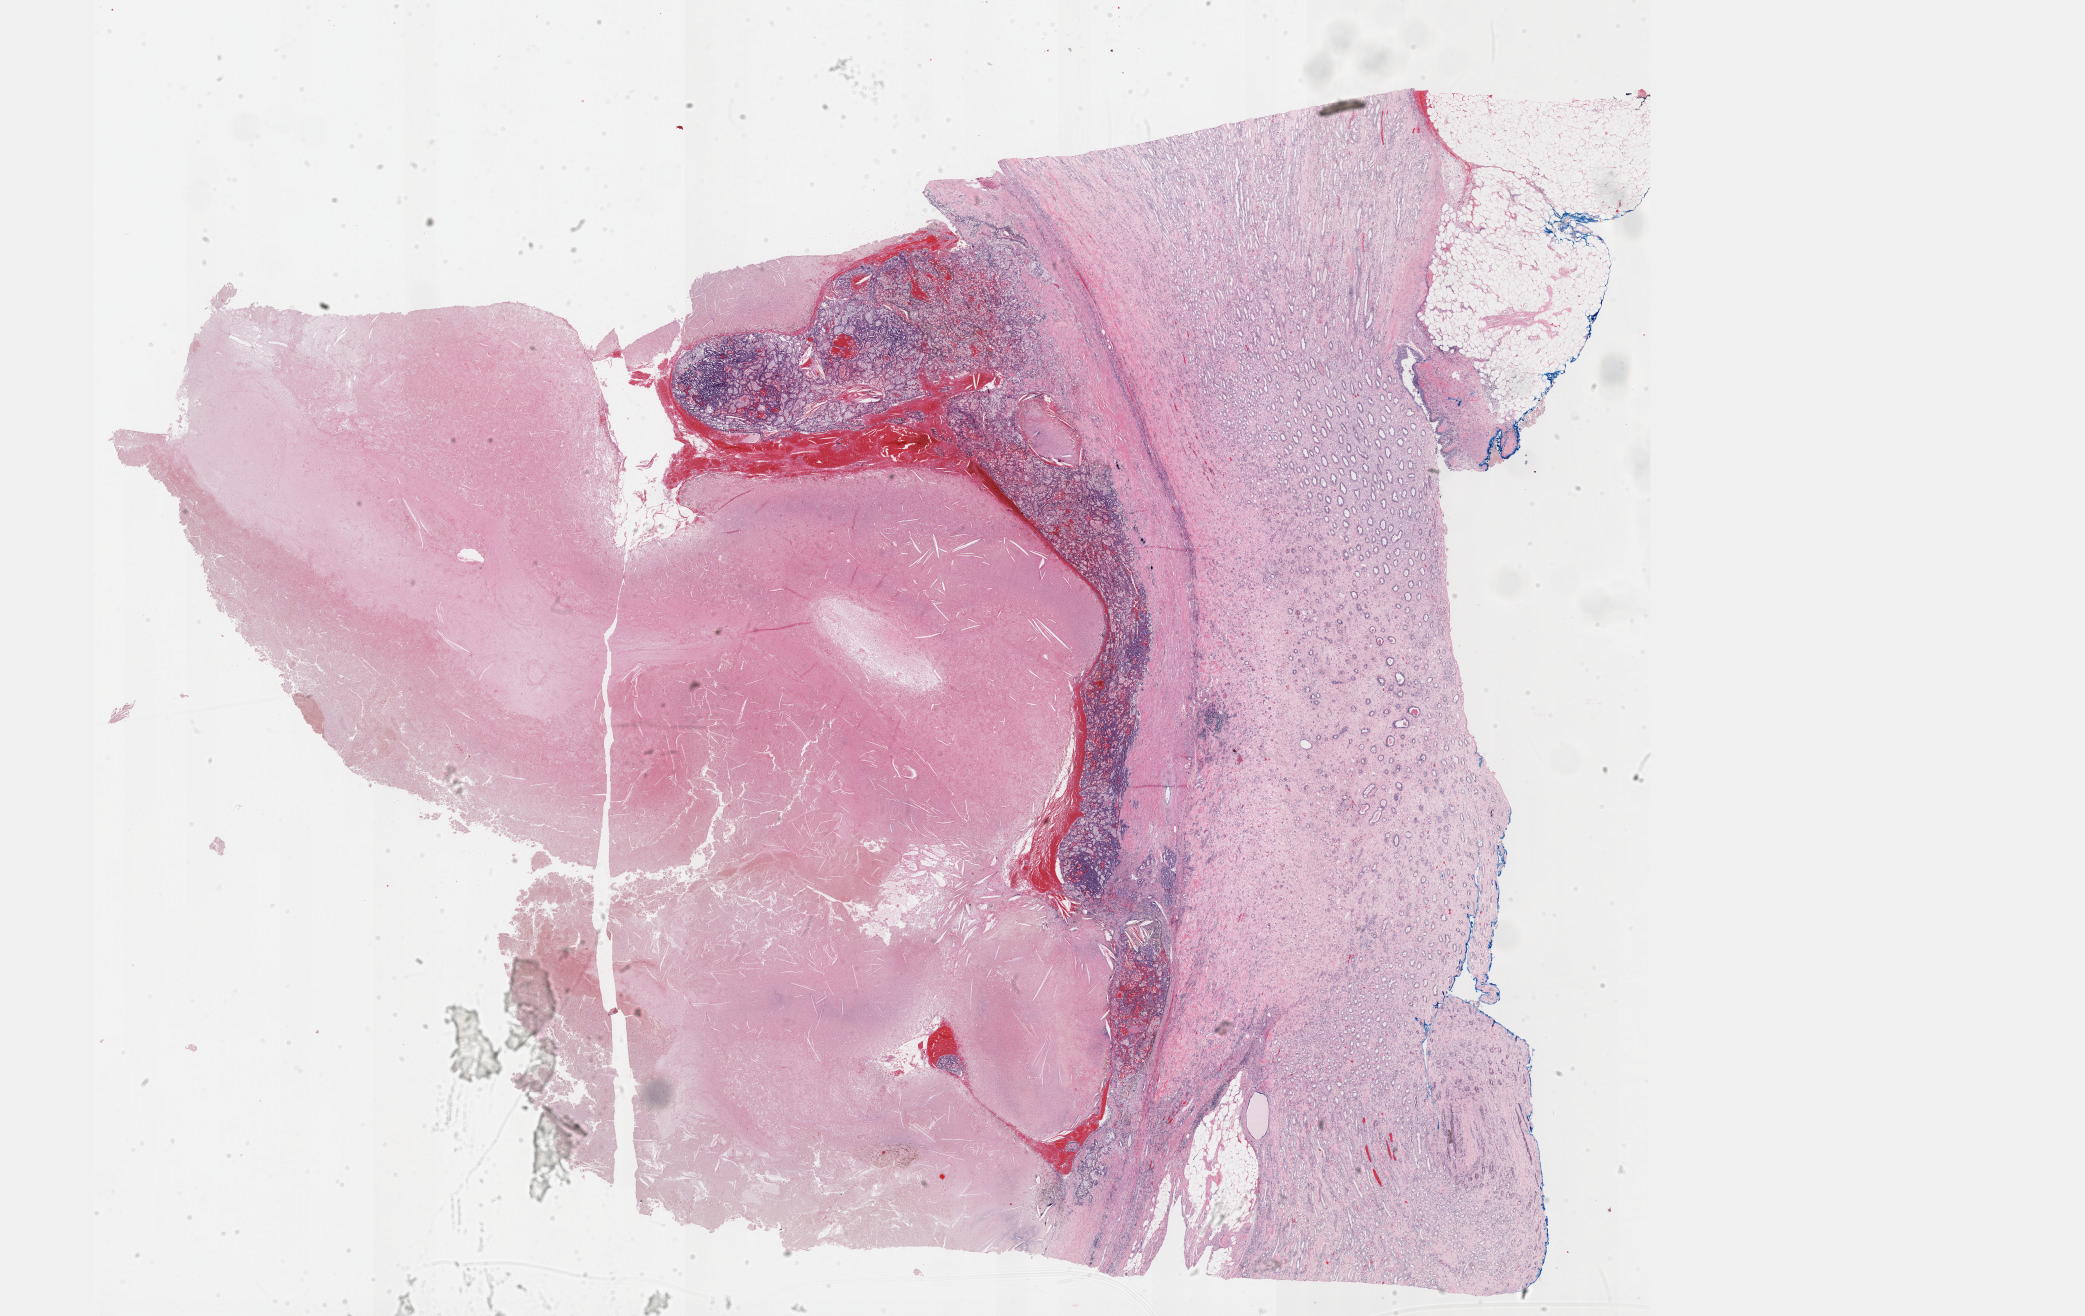
Digitized H&E-stained tissue section (whole slide), shown as a low-resolution overview of the whole scanned area (about 33.7 x 21.3 mm). FFPE section. Kidney, primary tumour sample. Male, age 85 years at initial diagnosis.
Laterality: right. AJCC pathologic stage: I. TNM: T1b NX M0. Diagnosis: Papillary adenocarcinoma, NOS.